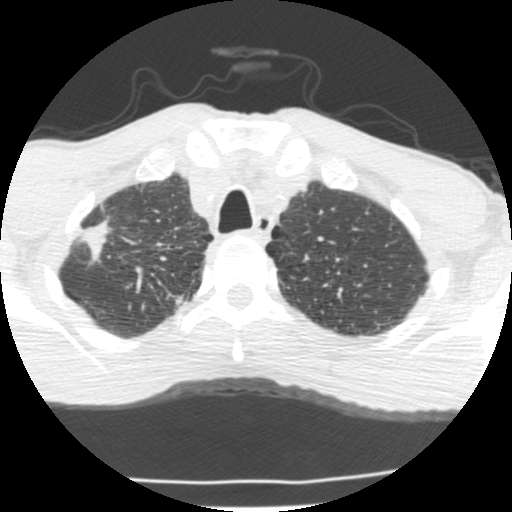
Axial slice from a low-dose chest CT screening exam; second screening round (one year after baseline); lung window (W 1500 / L -600 HU); 2.5 mm slice thickness; standard (soft-tissue) reconstruction kernel (STANDARD); slice 35 of 214 in the series. Male, age 62 years at enrolment.
Expert-annotated lung lesion, bounding box <58,214,133,271> (left, top, right, bottom; pixels). The exam's reader record, not a measurement of the box and not confirmed to be the same lesion: non-calcified nodule or mass ≥4 mm, right upper lobe, 23 × 11 mm, spiculated (stellate) margins, soft tissue attenuation, pre-existing on the prior screen: yes. Later outcome: lung cancer diagnosed 277 days after this screen — adenocarcinoma, NOS, right upper lobe, poorly differentiated (G3), stage IIA (AJCC 6th edition), 22 mm at pathology.